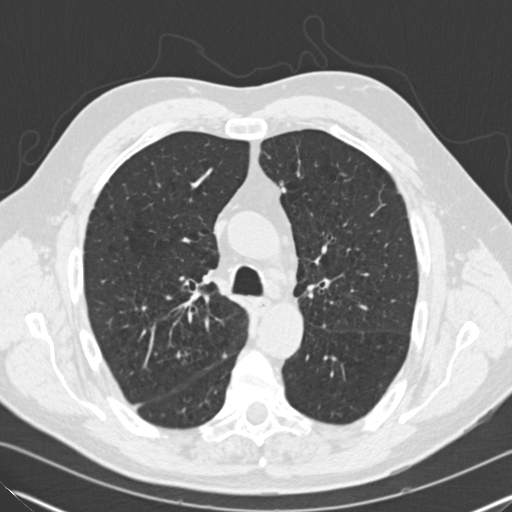
Chest CT (low-dose screening protocol), one axial image, baseline annual screen, lung window (W 1500 / L -600 HU), 2 mm slice thickness, 140 kVp. Male, age 65 years at enrolment. Former smoker at enrolment.
• Expert-annotated lung lesion, box from (x=159, y=340) to (x=200, y=376) px.
• The screening reader recorded 5 non-calcified nodules or masses ≥4 mm on this exam; which of them this box marks is not recorded.
• Official screen result: positive, change unspecified: nodule(s) >= 4 mm or enlarging nodule(s), mass(es), or other non-specific abnormalities suspicious for lung cancer.
• Participant outcome: lung cancer diagnosed 814 days after this screen — adenocarcinoma, NOS, right upper lobe, moderately differentiated (G2), stage IA (AJCC 6th edition), 16 mm at pathology.